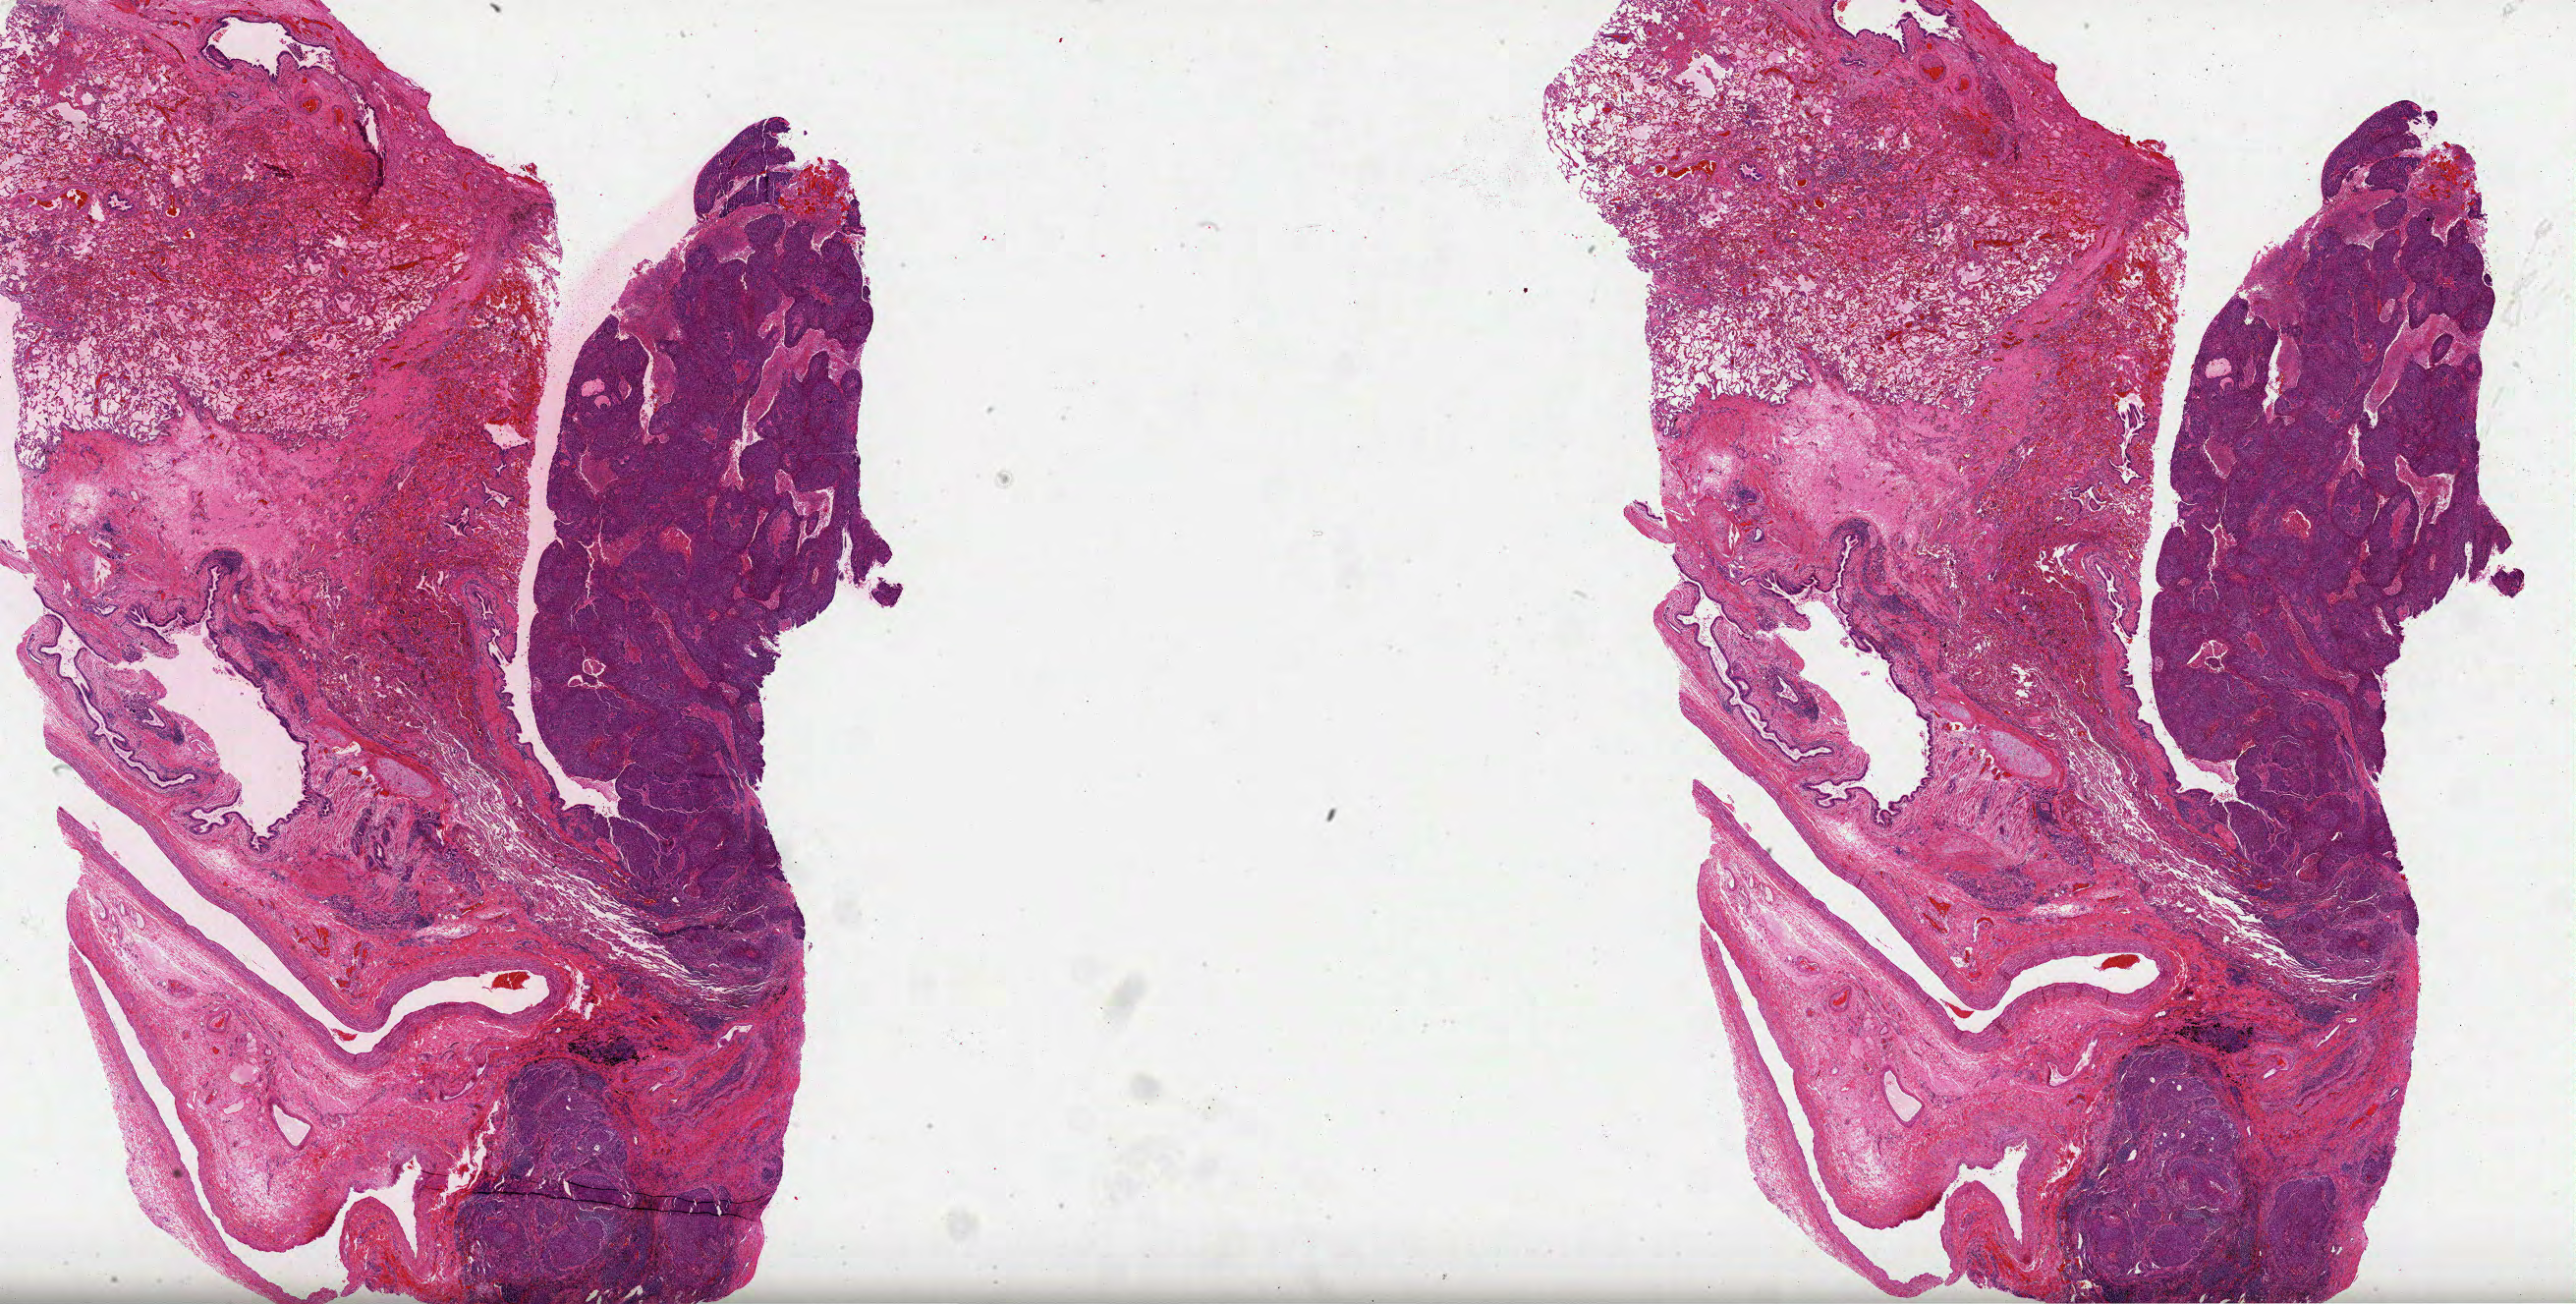
Digitized Hematoxylin and eosin (H&E) stained tissue section (whole slide), shown as a low-resolution overview of the whole scanned area (about 42.3 x 21.4 mm), formalin-fixed paraffin-embedded (FFPE) diagnostic section, primary tumour sample from the lung. Male, age 66 years at initial diagnosis.
Pathologic diagnosis: Squamous cell carcinoma, NOS (upper lobe, lung). AJCC pathologic stage: IIIA (6th edition).